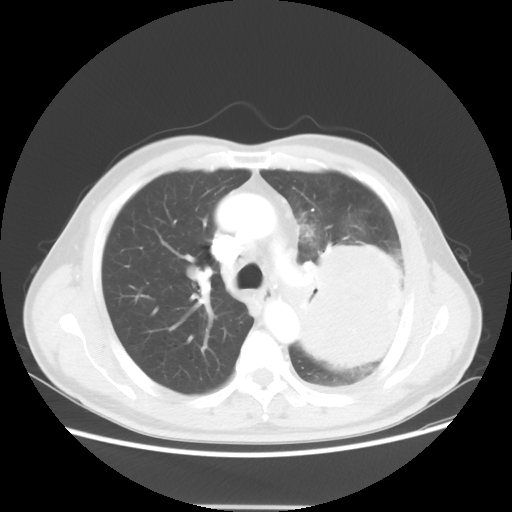
Chest CT, one axial slice; slice 36 of 53 in the series (ordered by position); reconstruction kernel STANDARD; 100 kVp; lung window (W 1500 / L -600 HU); 512 × 512 image matrix, field of view 391 × 391 mm. Male patient, age 60 years. Case-level facts recorded for this patient, not image findings: clinical TNM (as recorded): T4 N1 M1a.
Structures marked on this image (rectangle marked by the reading radiologist):
- lung tumour (recorded histology: large cell carcinoma): bounding box <293,242,408,376> (left, top, right, bottom; pixels)